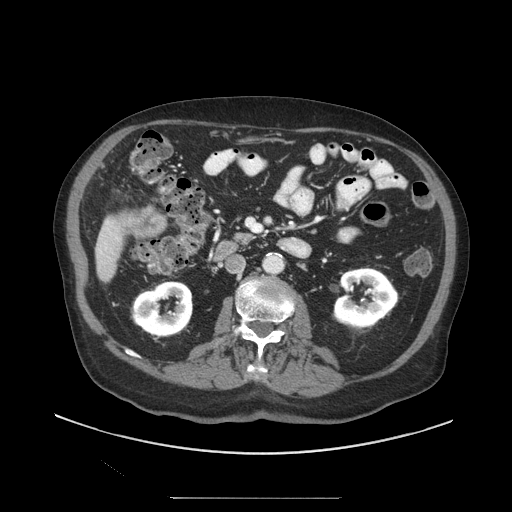
Contrast-enhanced abdominal CT (liver protocol), one axial slice; soft-tissue window (W 400 / L 40 HU); 2.5 mm slice thickness; 512 × 512 image matrix, field of view 450 × 450 mm. Case-level facts recorded for this patient, not image findings: diagnosis: hepatocellular carcinoma (patient treated with transarterial chemoembolisation; whether this scan precedes or follows treatment is not stated here); TNM stage (as recorded): Stage-IIIC; Child-Pugh class: A; tumour differentiation: well differentiated; tumour nodularity: uninodular.
Outlined on this slice (semi-automatic segmentation, software-assisted and operator-edited):
- liver parenchyma outside the tumour (the mass and vessels are separate outlines, so this box may not span the whole liver): bounding box <94,216,124,282> (left, top, right, bottom; pixels)
- liver vessels: <100,251,102,253>